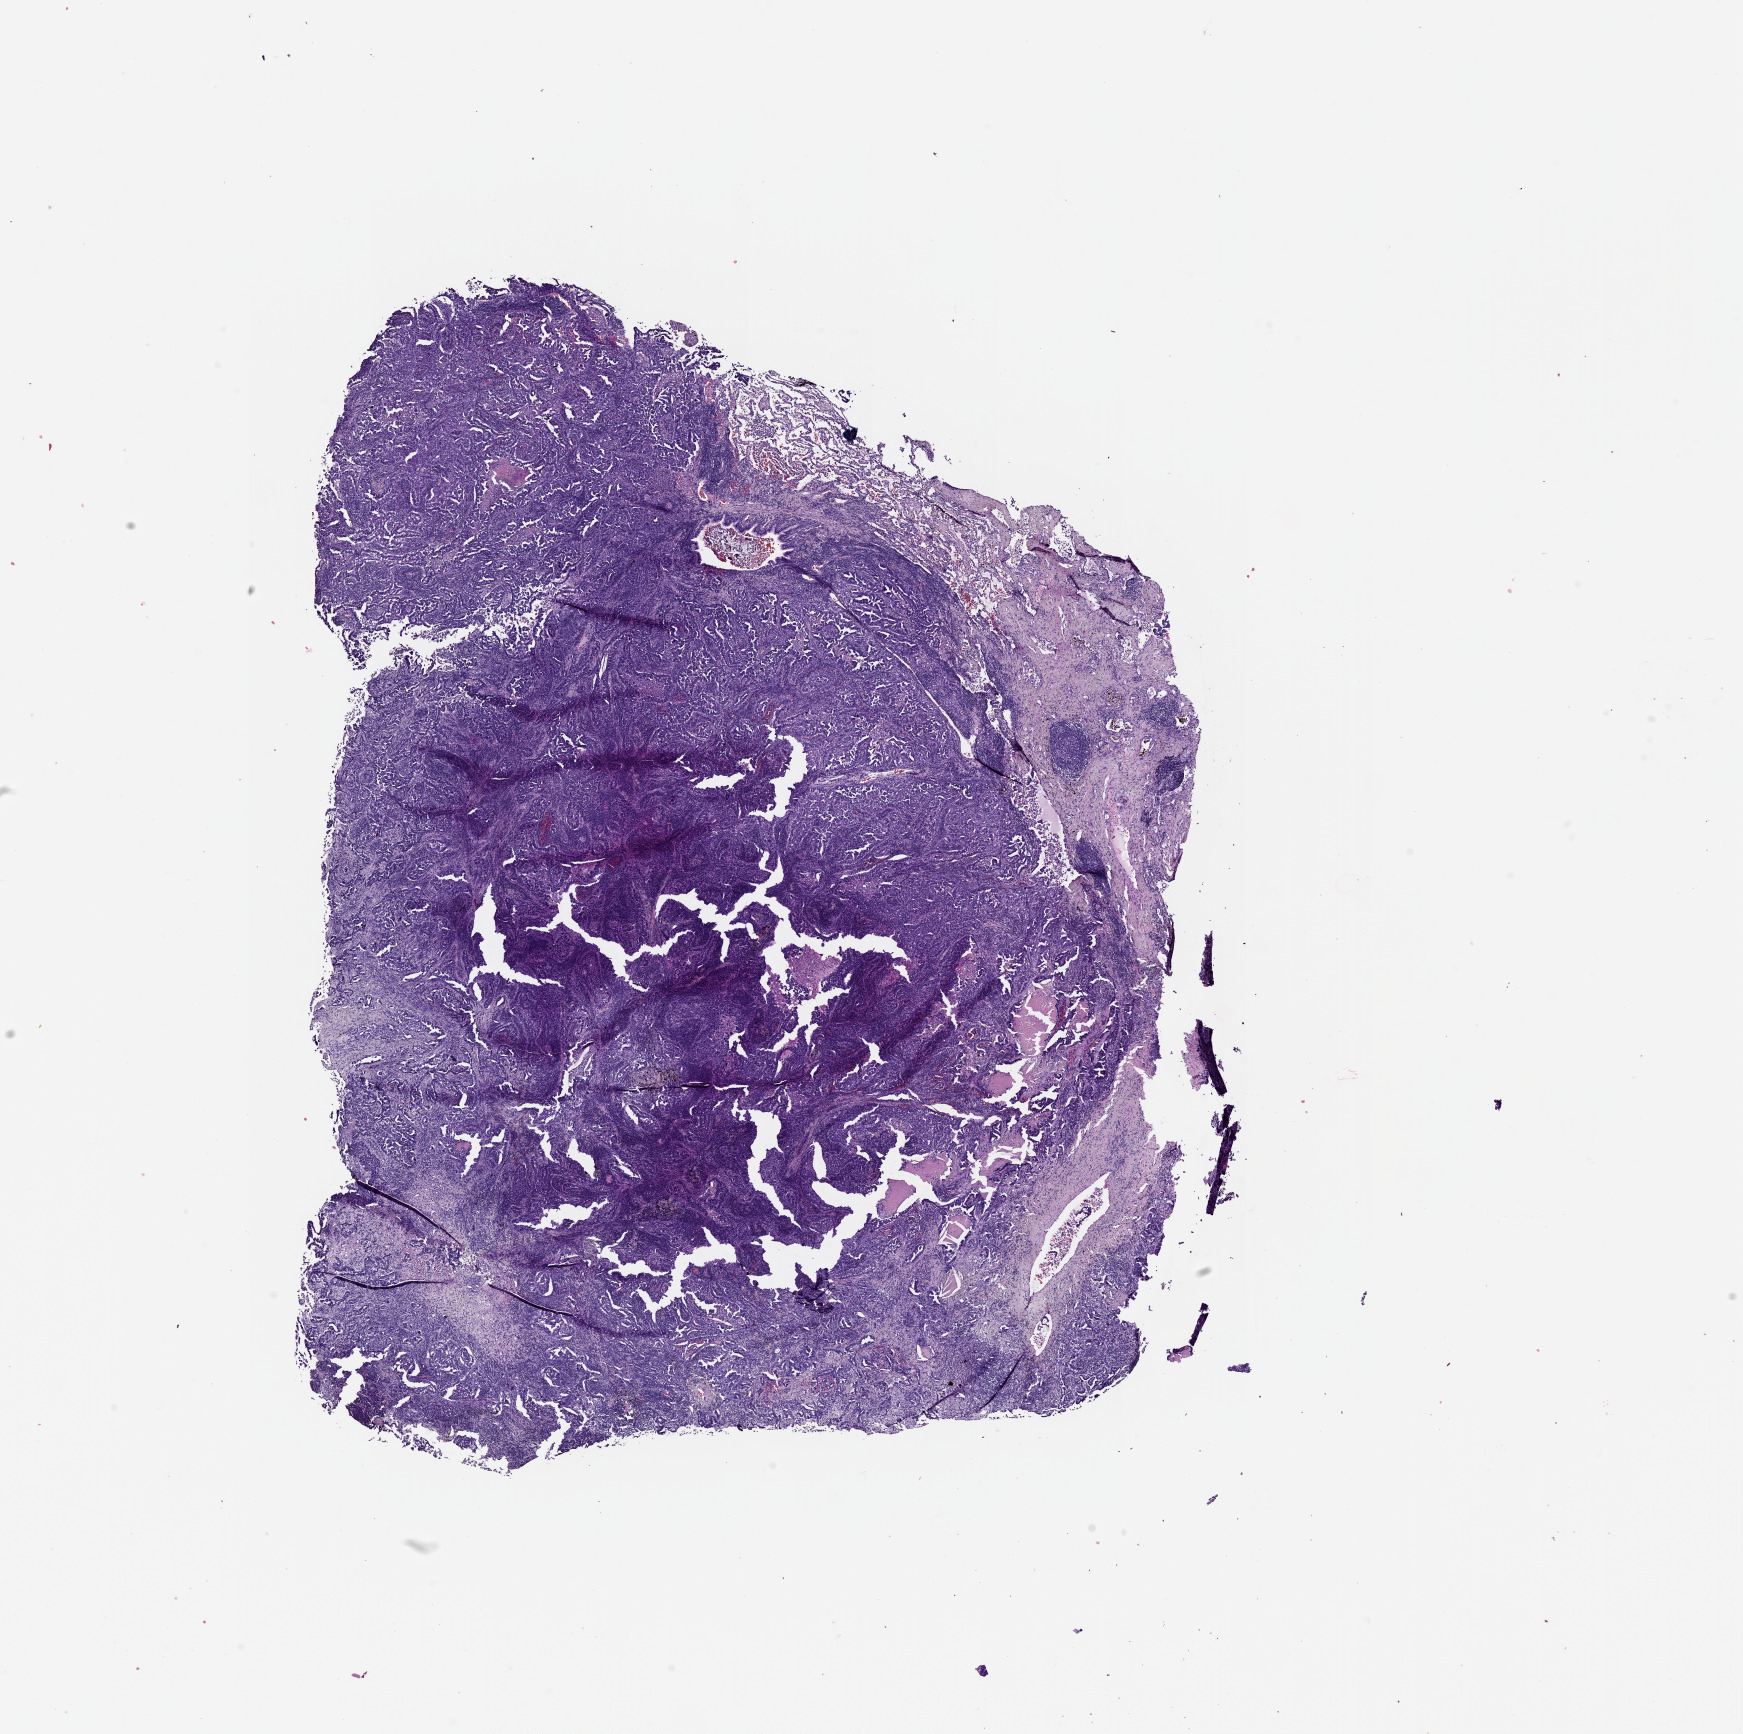
Digitized H&E tissue section (whole slide), whole scanned area (about 14.0 x 14.0 mm, acquisition: 20x scan) shown as a low-resolution overview. Lung, tumour tissue. 68-year-old male patient. Histologic grade: G1 (well differentiated).
AJCC pathologic stage: IB. Diagnosis: Adenocarcinoma, NOS.